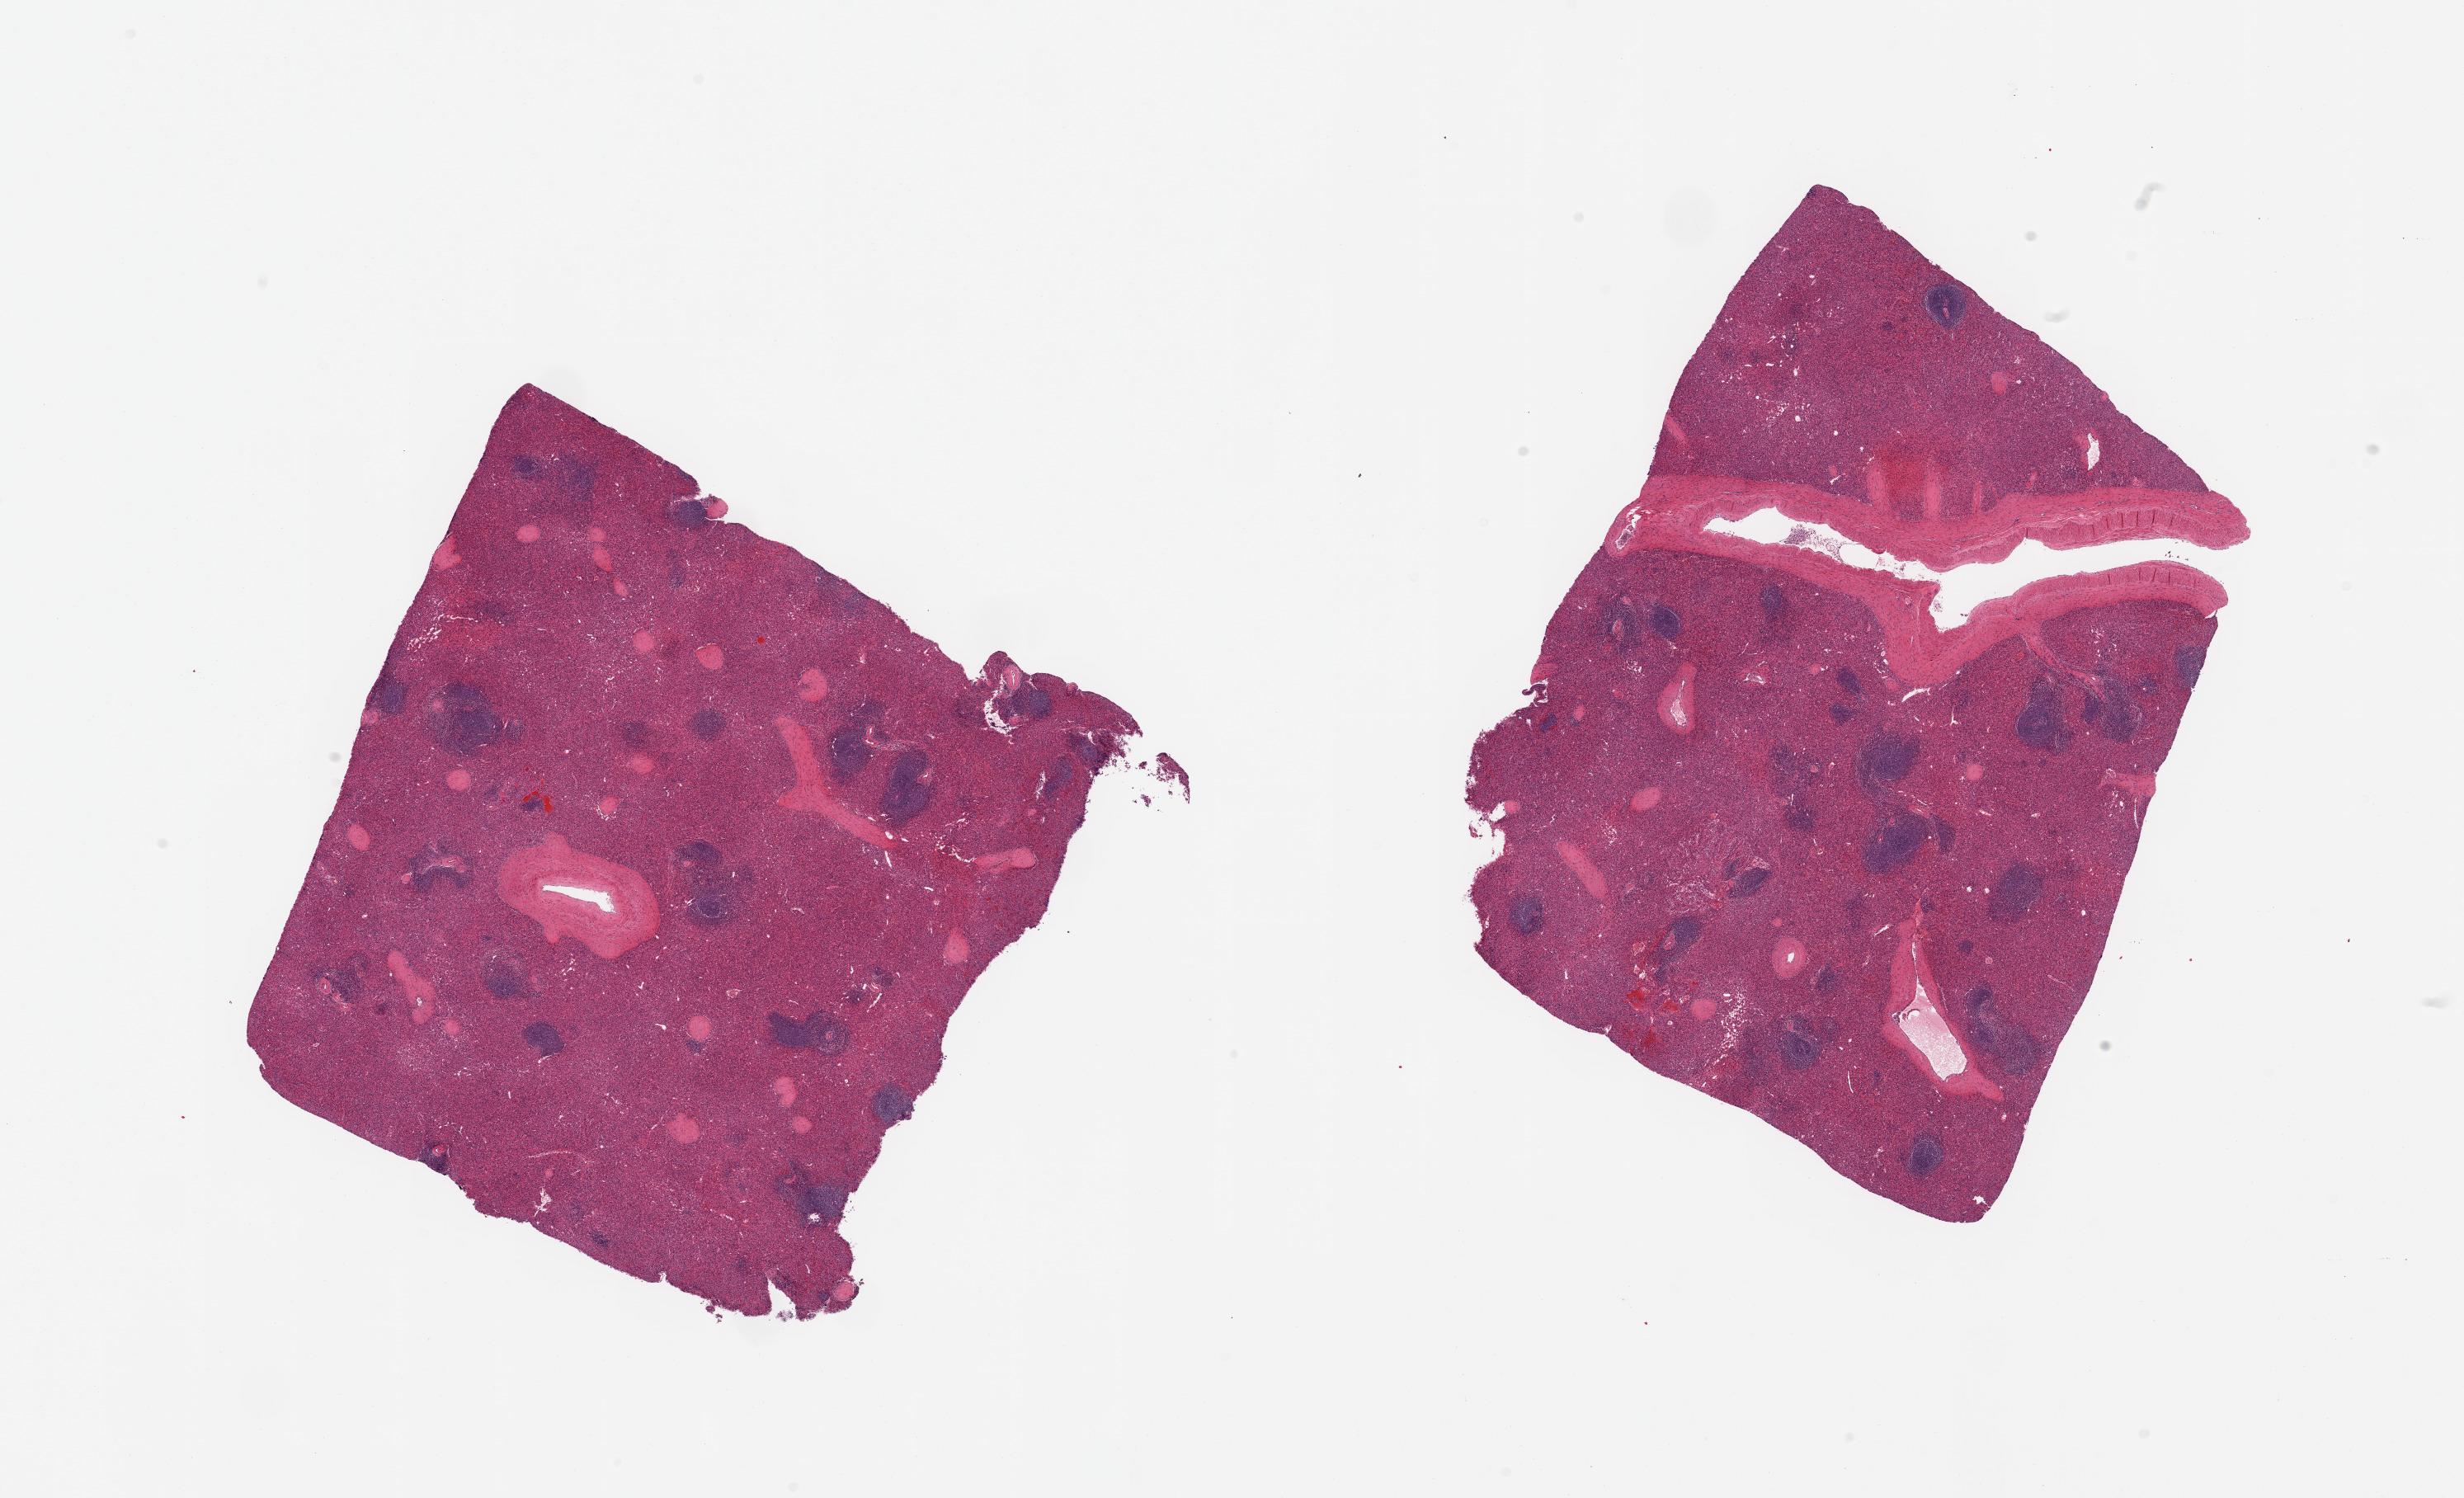
Digitized haematoxylin and eosin-stained section, shown as a low-resolution overview of the whole scanned area (about 23.6 x 14.4 mm, slide scanned at 20x); PAXgene-fixed paraffin-embedded (PFPE) section; target tissue: spleen; donor tissue sample. Donor: male.
- review note (as recorded): 2 pieces; minimal congestion; well defined lymphoid tissue